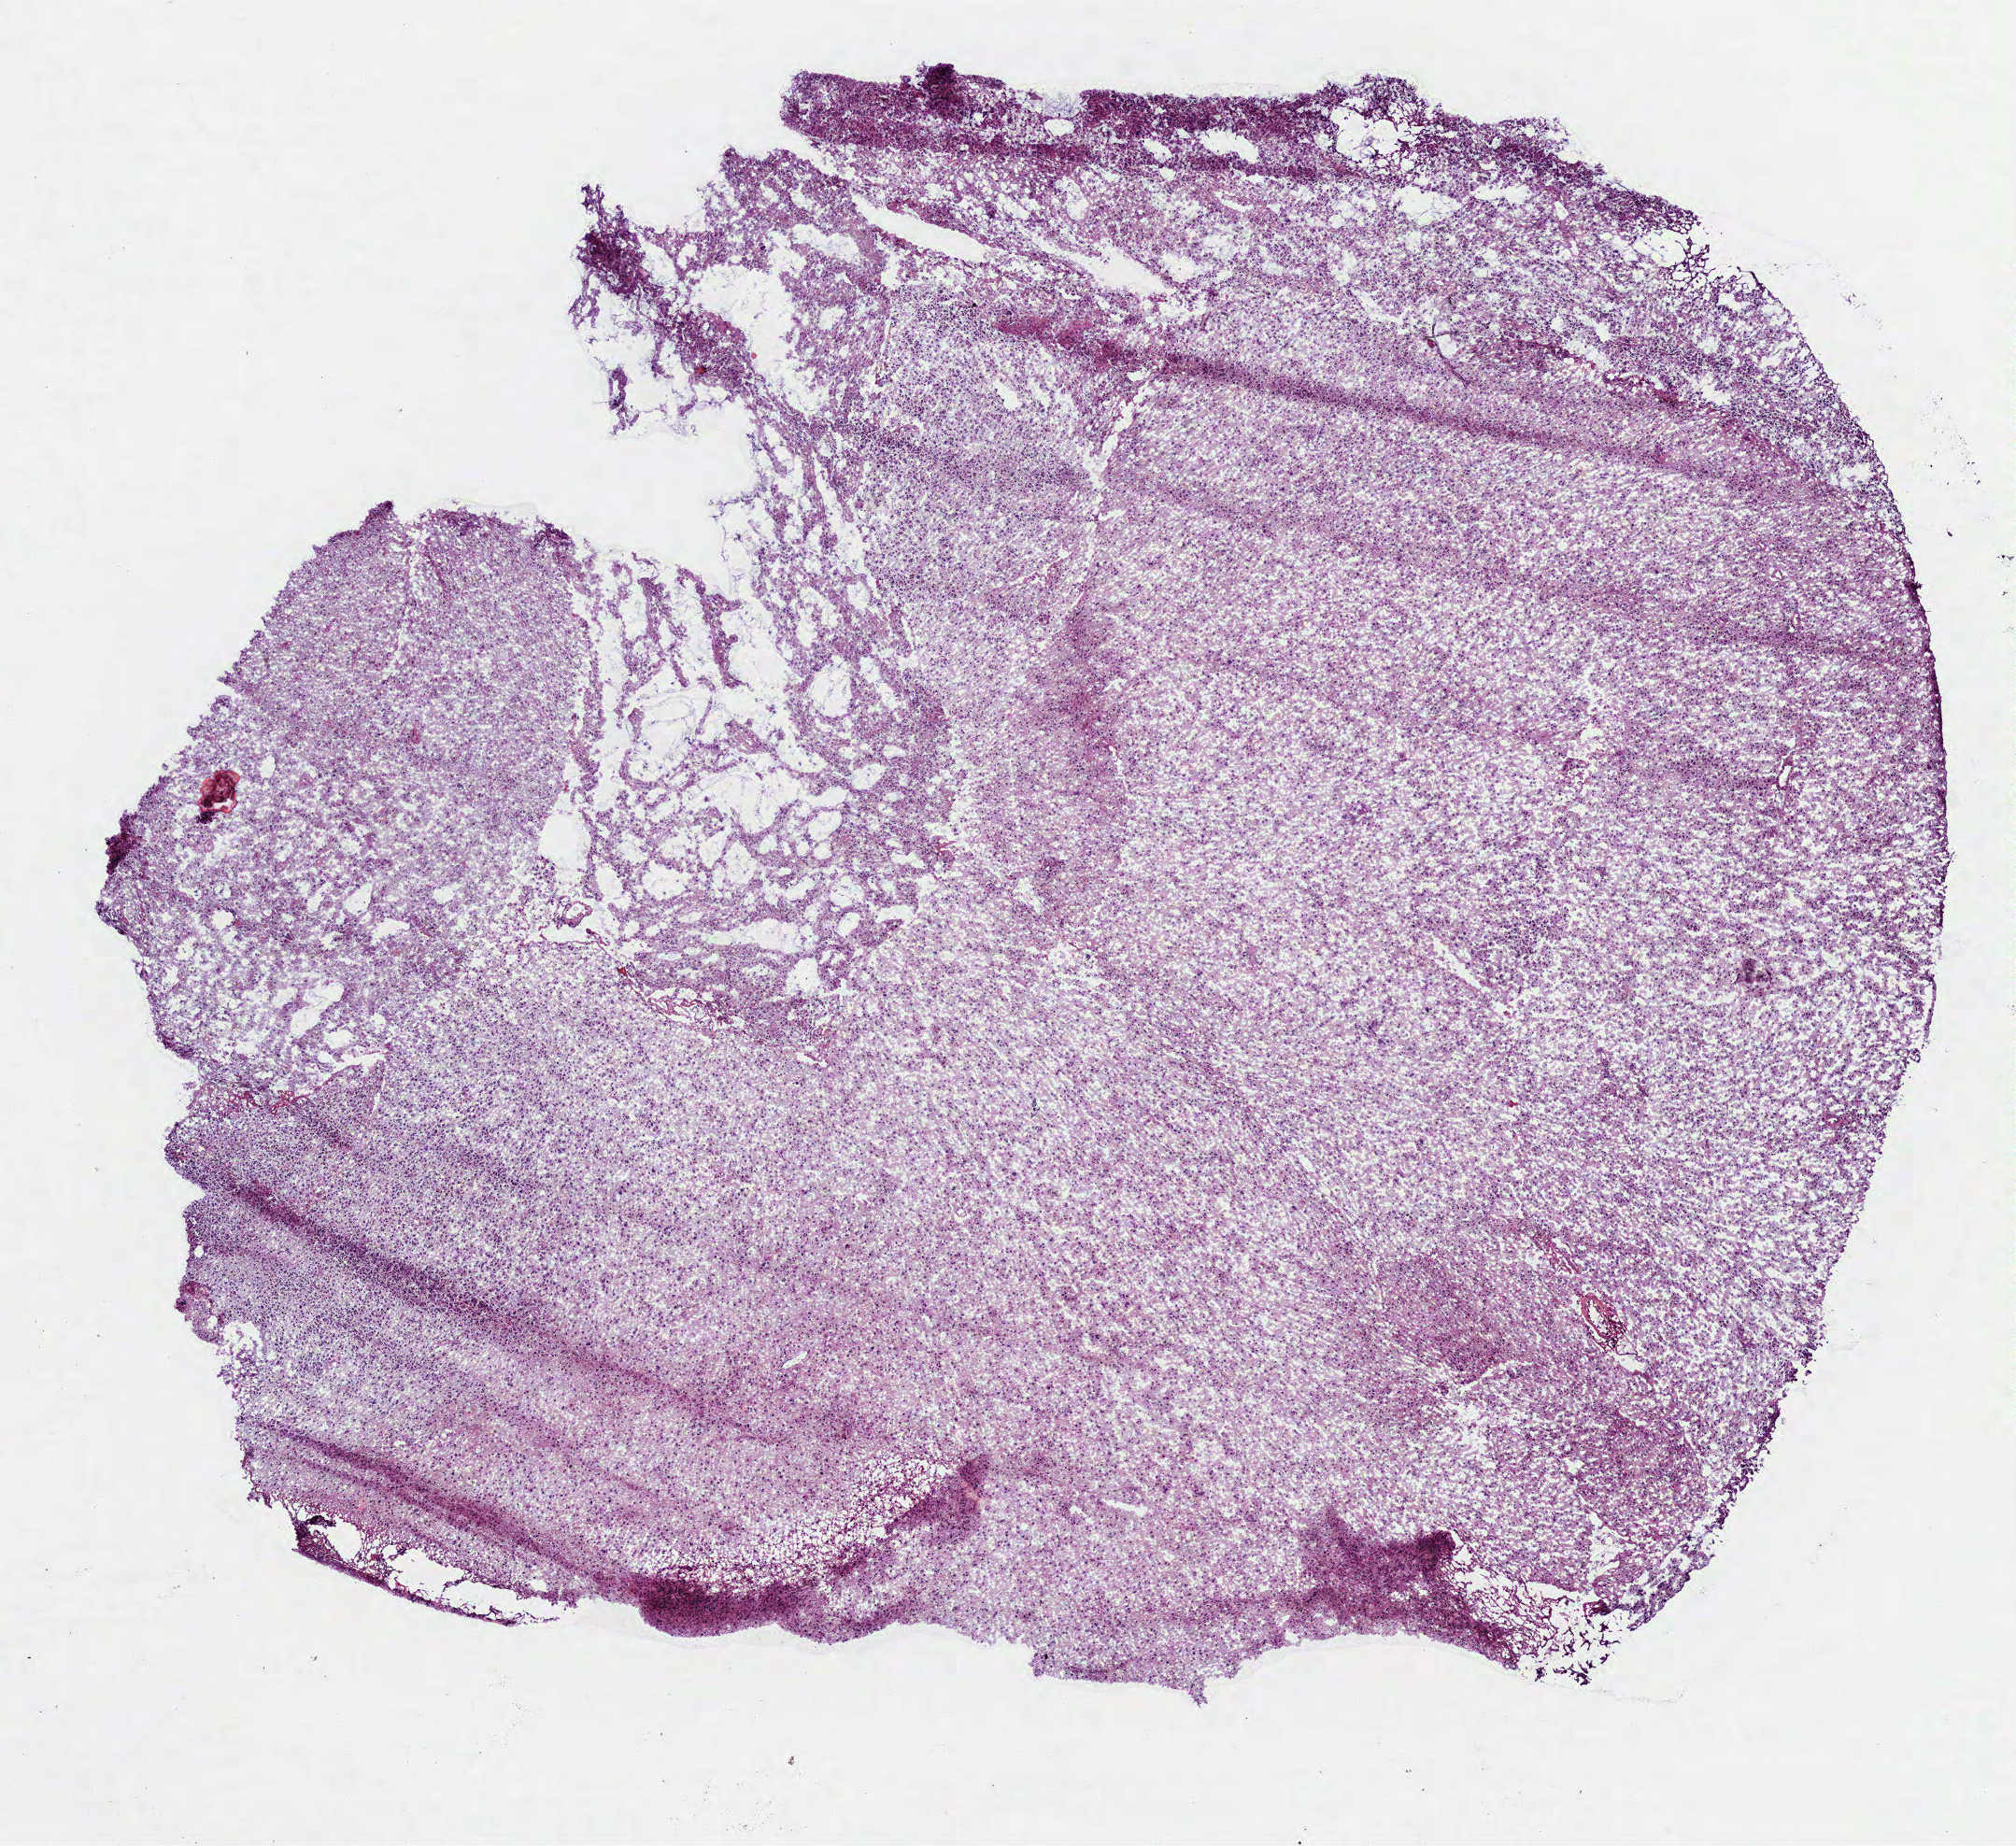
H&E-stained whole-slide image, low-resolution overview of the scanned area, about 8.7 x 8.0 mm, frozen section, sample: primary tumour, brain. Patient: female, age at initial diagnosis 41 years. Histologic grade: G2 (moderately differentiated). Composition of this section per pathologist review: tumour cells 100%, tumour nuclei 70%, normal cells 0%, stromal cells 0%, necrosis 0%.
- histologic diagnosis: Oligodendroglioma, NOS (cerebrum)